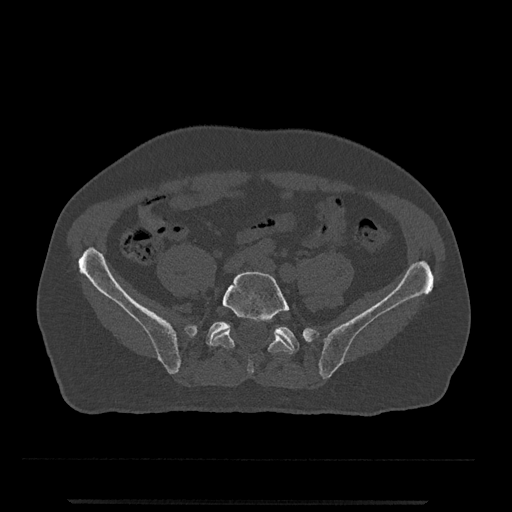
CT including the spine, one axial slice; reconstruction kernel Br40s/3; 120 kVp; bone window (W 1800 / L 400 HU); 0.5 mm slice thickness; 512 × 512 image matrix. Male patient, age 63 years. Case-level facts recorded for this patient, not image findings: primary cancer: prostate.
Annotated regions visible in this slice (semi-automatically segmented with operator editing):
- L5 vertebra: bounding box <210,271,293,374> (left, top, right, bottom; pixels)